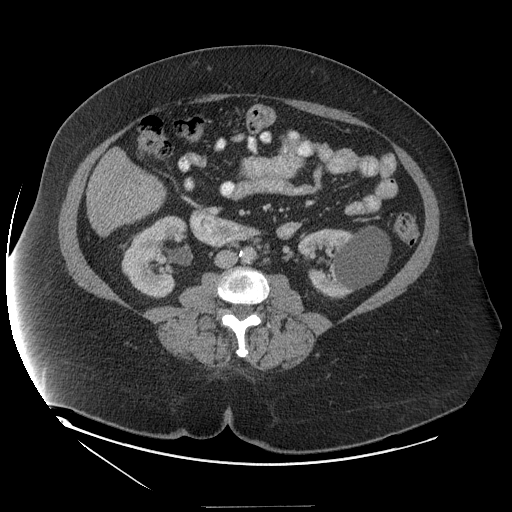
Contrast-enhanced abdominal CT (liver protocol), one axial slice. Position 32 of 127 along the scan axis. 140 kVp. Soft-tissue window (W 400 / L 40 HU). 2.5 mm slice thickness. 512 × 512 image matrix, field of view 480 × 480 mm. From the clinical record (not read from this slice): diagnosis: hepatocellular carcinoma (patient treated with transarterial chemoembolisation; whether this scan precedes or follows treatment is not stated here); TNM stage (as recorded): Stage-II; Child-Pugh class: A; tumour differentiation: well differentiated; tumour nodularity: multinodular.
Structures marked on this image (semi-automatically segmented with operator editing):
- liver parenchyma outside the tumour (the mass and vessels are separate outlines, so this box may not span the whole liver): bounding box [x1, y1, x2, y2] px = [86, 178, 164, 234]